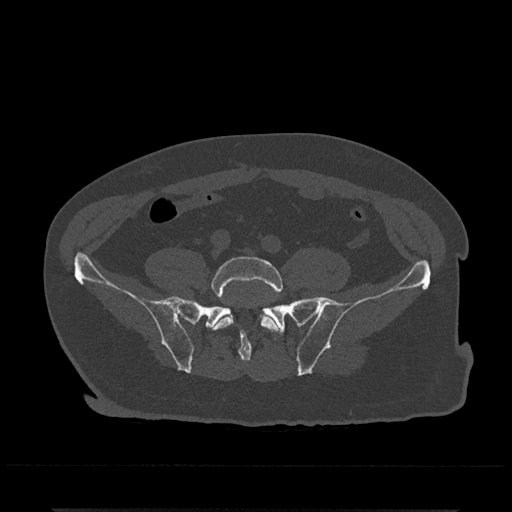
CT including the spine, one axial slice; bone window (W 1800 / L 400 HU); 0.5 mm slice thickness; 512 × 512 image matrix, field of view 393 × 393 mm. Patient: male, 67 years. From the clinical record (not read from this slice): primary cancer: prostate.
Annotated regions visible in this slice (semi-automatically segmented with operator editing):
- L5 vertebra: bounding box [x1, y1, x2, y2] px = [208, 256, 283, 332]